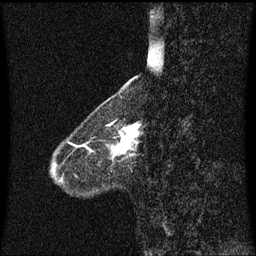
Breast MRI (dynamic contrast-enhanced), one sagittal slice; slice 19 of 60 in the series (ordered by position); dynamic contrast-enhanced series, image 2 of 3 at this slice position (ordered by acquisition); 1.5 T; TE 4.2 ms, TR 8.4 ms; 2 mm slice thickness; 256 × 256 image matrix, field of view 200 × 200 mm. Patient: female, 58 years.
Annotated regions visible in this slice (semi-automatically segmented with operator editing):
- analysis volume of interest (the breast-tissue region the enhancement analysis was run in; not a lesion): bounding box <108,122,141,160> (left, top, right, bottom; pixels)
- tumour enhancement mask (voxels above the 70 % enhancement threshold inside the analysis volume of interest): <110,123,139,155>